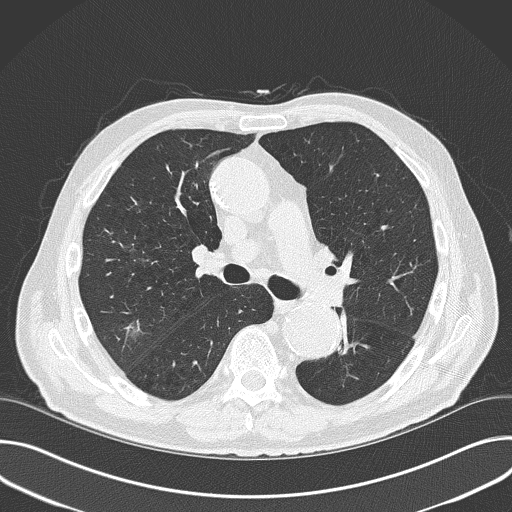
Low-dose screening chest CT, one axial slice. Position 99 of 177 along the scan axis. Reconstruction kernel B50f. 120 kVp. Lung window (W 1500 / L -600 HU). 2 mm slice thickness. 512 × 512 image matrix.
Outlined on this slice (manually delineated by an expert):
- lesion 1 (tumor, upper lobe of right lung): bounding box (x1, y1, x2, y2) in pixels: (130, 328, 139, 329)